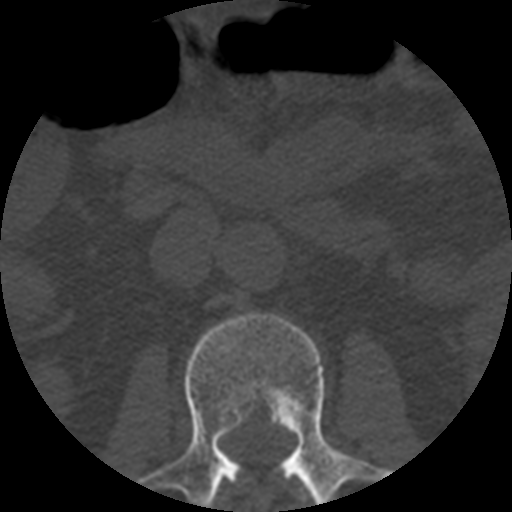
CT including the spine, one axial slice; slice 155 of 508 in the series (ordered by position); reconstruction kernel STANDARD; bone window (W 1800 / L 400 HU); 512 × 512 image matrix, field of view 160 × 160 mm. Patient age 57 years. Case-level facts recorded for this patient, not image findings: primary cancer: prostate.
Structures marked on this image (semi-automatic segmentation, software-assisted and operator-edited):
- L1 vertebra: box from (x=301, y=494) to (x=312, y=502) px
- L2 vertebra: (x=138, y=313)–(x=392, y=506)